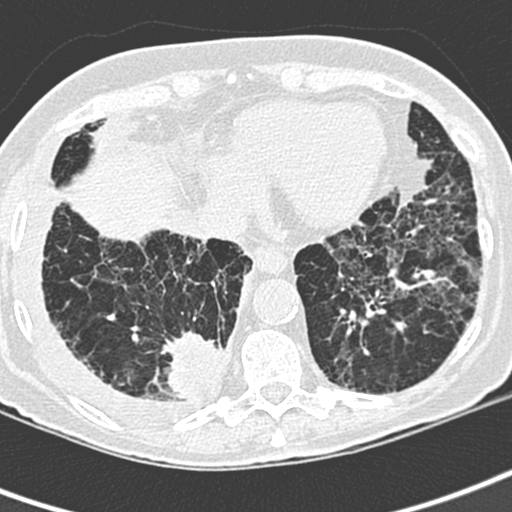
Low-dose screening chest CT, one axial slice. Lung window (W 1500 / L -600 HU). 1.3 mm slice thickness. 512 × 512 image matrix.
Outlined on this slice (outlined manually by an expert reader):
- lesion 1 (tumor, lower lobe of right lung): bounding box (x1, y1, x2, y2) in pixels: (162, 332, 223, 399)